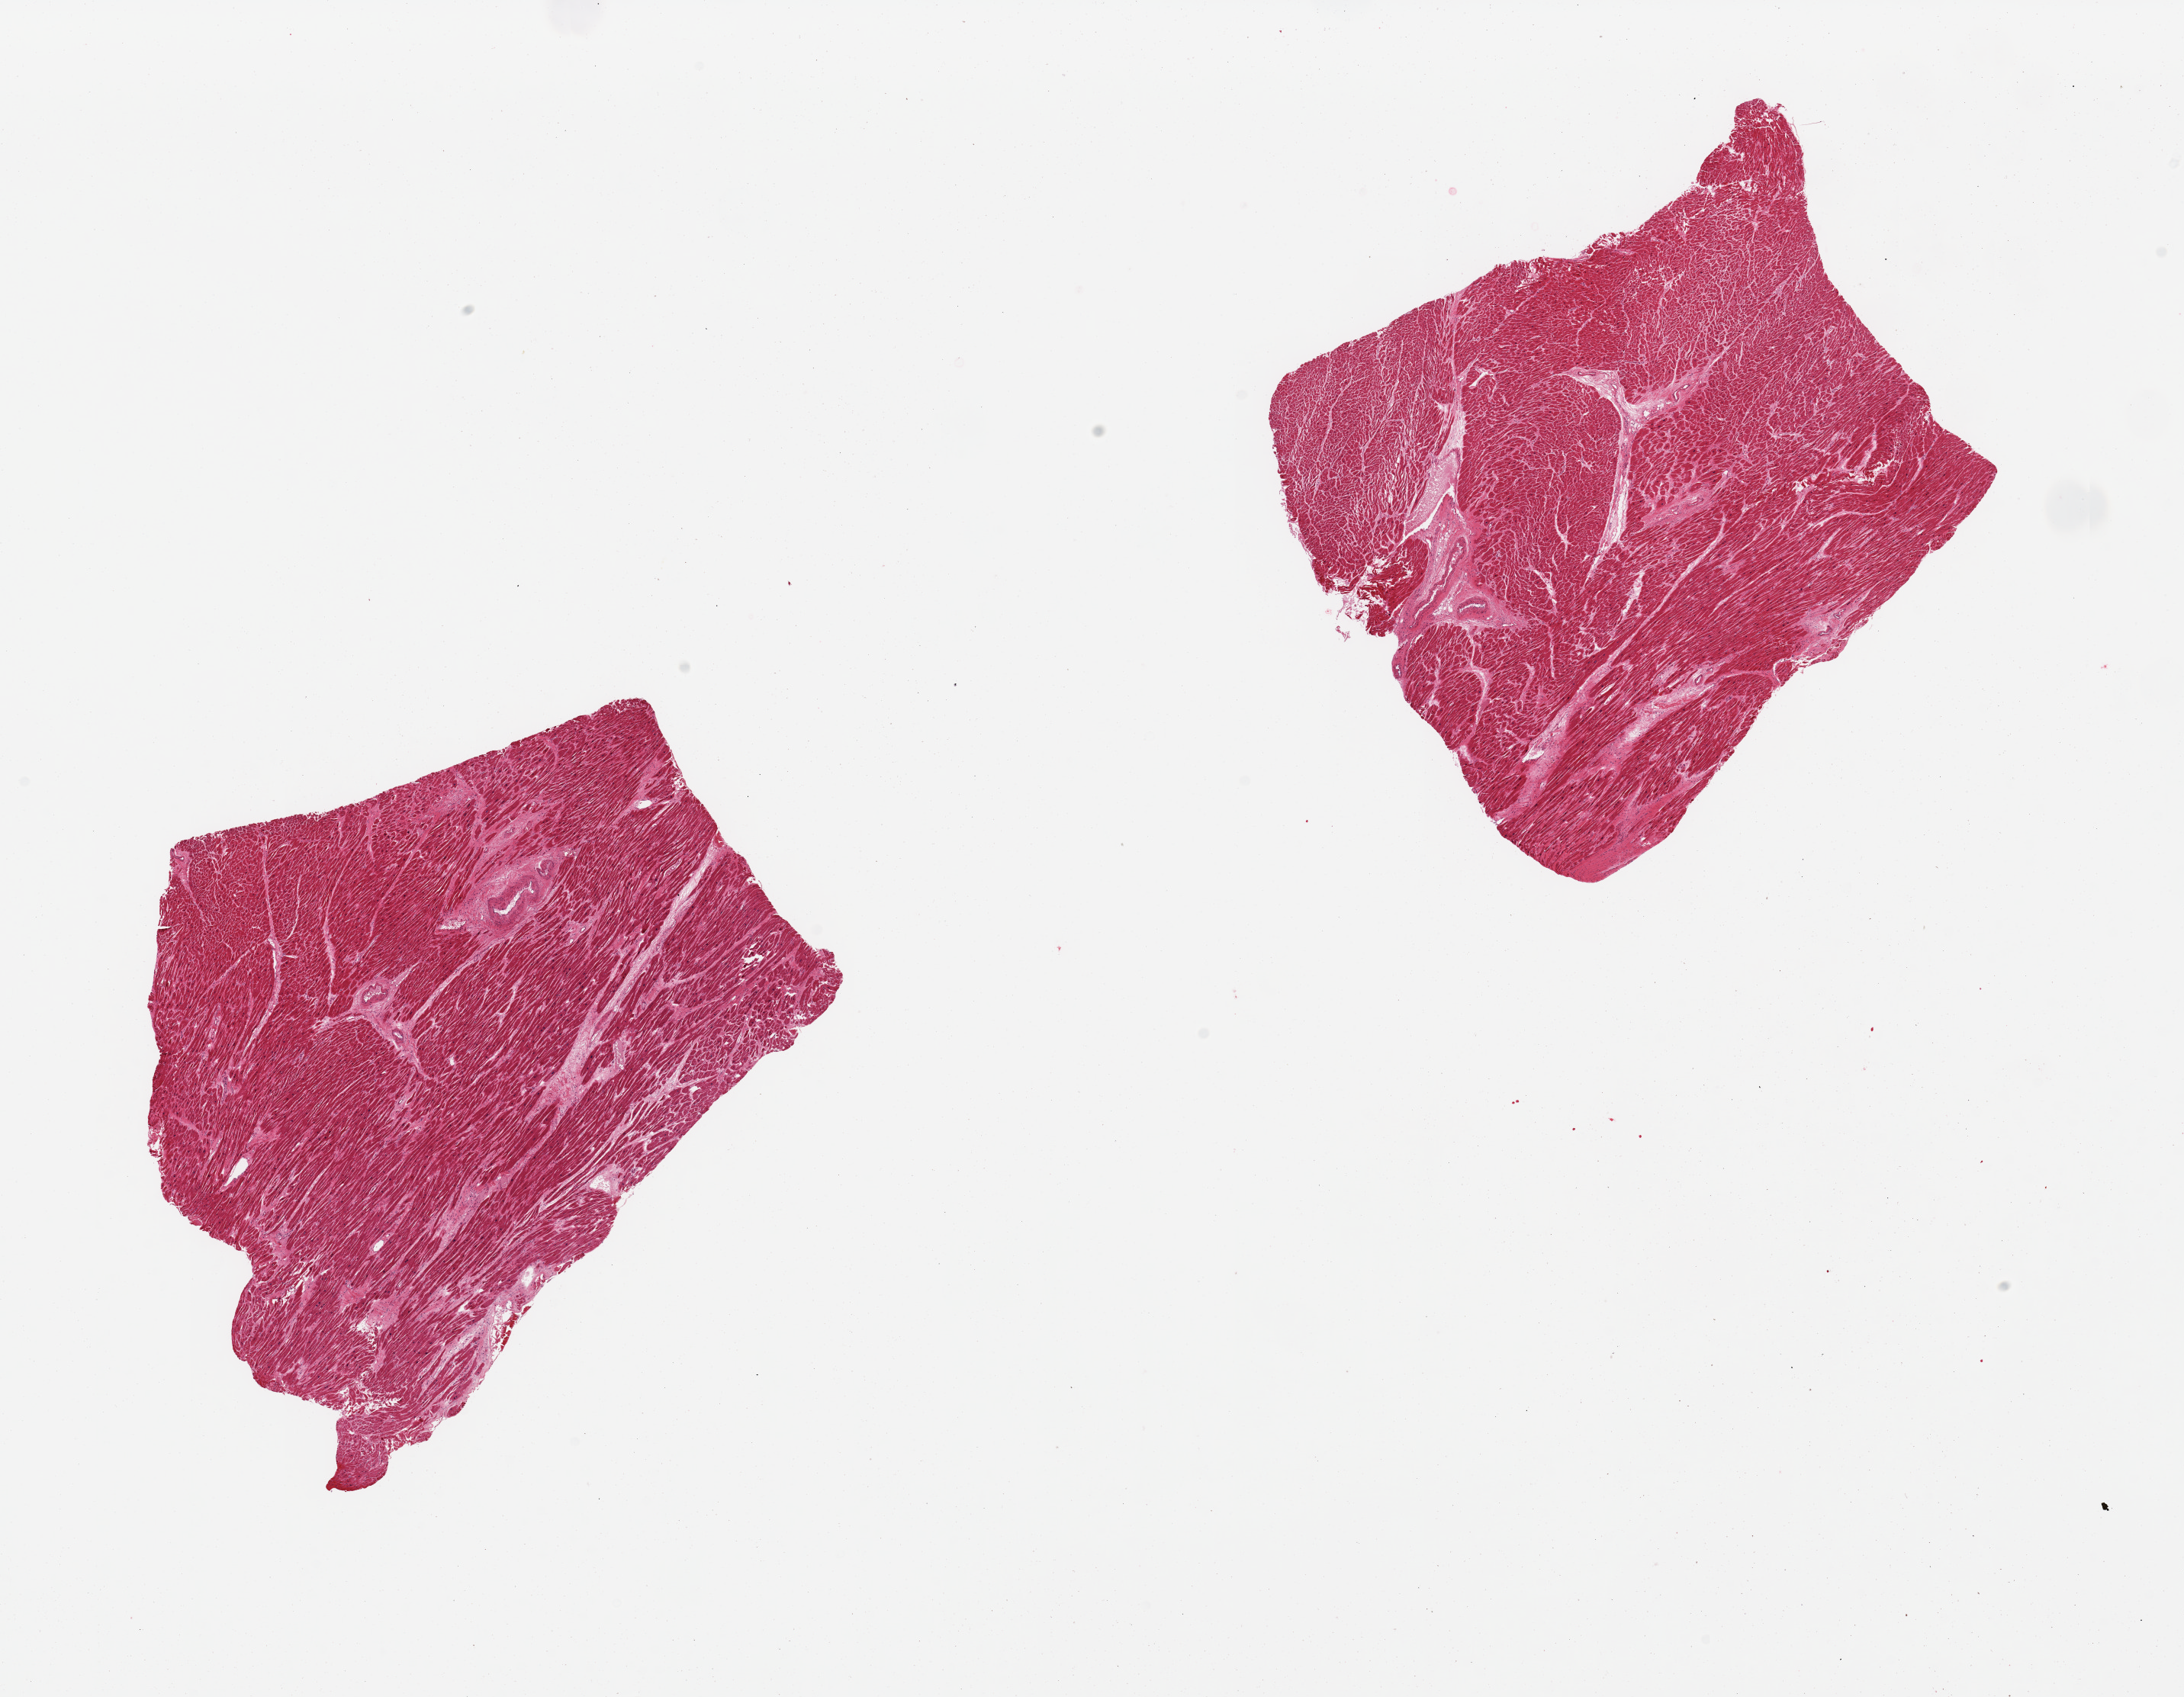
Haematoxylin and eosin whole-slide image, brightfield — shown as a low-resolution overview of the whole scanned area (about 22.6 x 17.6 mm). PAXgene-fixed paraffin-embedded (PFPE) section. Sampled site (target tissue): heart. Donor tissue sample. Donor: male.
Reviewer comment on this tissue sample: 2 pieces, moderate chronic ischemic changes/interstitial fibrosis.